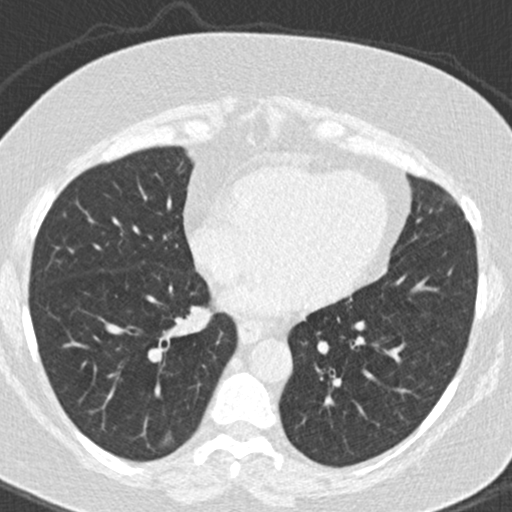
Low-dose screening chest CT, one axial slice. Position 68 of 177 along the scan axis. Reconstruction kernel B30f. 120 kVp. Lung window (W 1500 / L -600 HU). 2 mm slice thickness. 512 × 512 image matrix, field of view 300 × 300 mm.
Structures marked on this image (expert manual segmentation):
- lesion 1 (tumor, lower lobe of right lung): bounding box <161,430,173,447> (left, top, right, bottom; pixels)